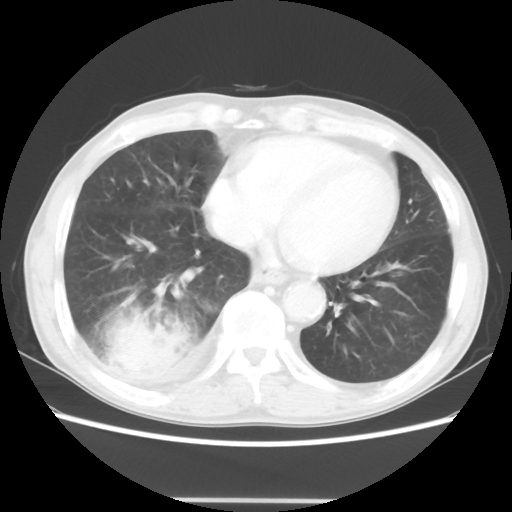
Chest CT, one axial slice; position 13 of 48 along the scan axis; lung window (W 1500 / L -600 HU); 5 mm slice thickness; 512 × 512 image matrix, field of view 361 × 361 mm. Male patient, age 66 years. Case-level facts recorded for this patient, not image findings: clinical TNM (as recorded): T4 N1 M1; histopathological grade: G3.
Annotated regions visible in this slice (bounding box drawn by a radiologist):
- lung tumour (recorded histology: small cell carcinoma): bounding box <100,297,192,392> (left, top, right, bottom; pixels)